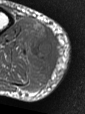
MRI of an extremity soft-tissue mass, one axial slice. Slice 14 of 47 in the series (ordered by position). MR volume resampled by the dataset authors to the PET/CT grid (not the native acquisition matrix). 85 × 114 image matrix. Male patient. Case-level facts recorded for this patient, not image findings: histological type: pleiomorphic liposarcoma; grade: high; site of the primary tumour: right calf.
Outlined on this slice (expert contour drawn on MRI and transferred to this co-registered scan by the dataset authors):
- gross tumour volume including surrounding oedema: bounding box (x1, y1, x2, y2) in pixels: (26, 25, 59, 88)
- gross tumour volume (mass): (31, 37, 53, 61)